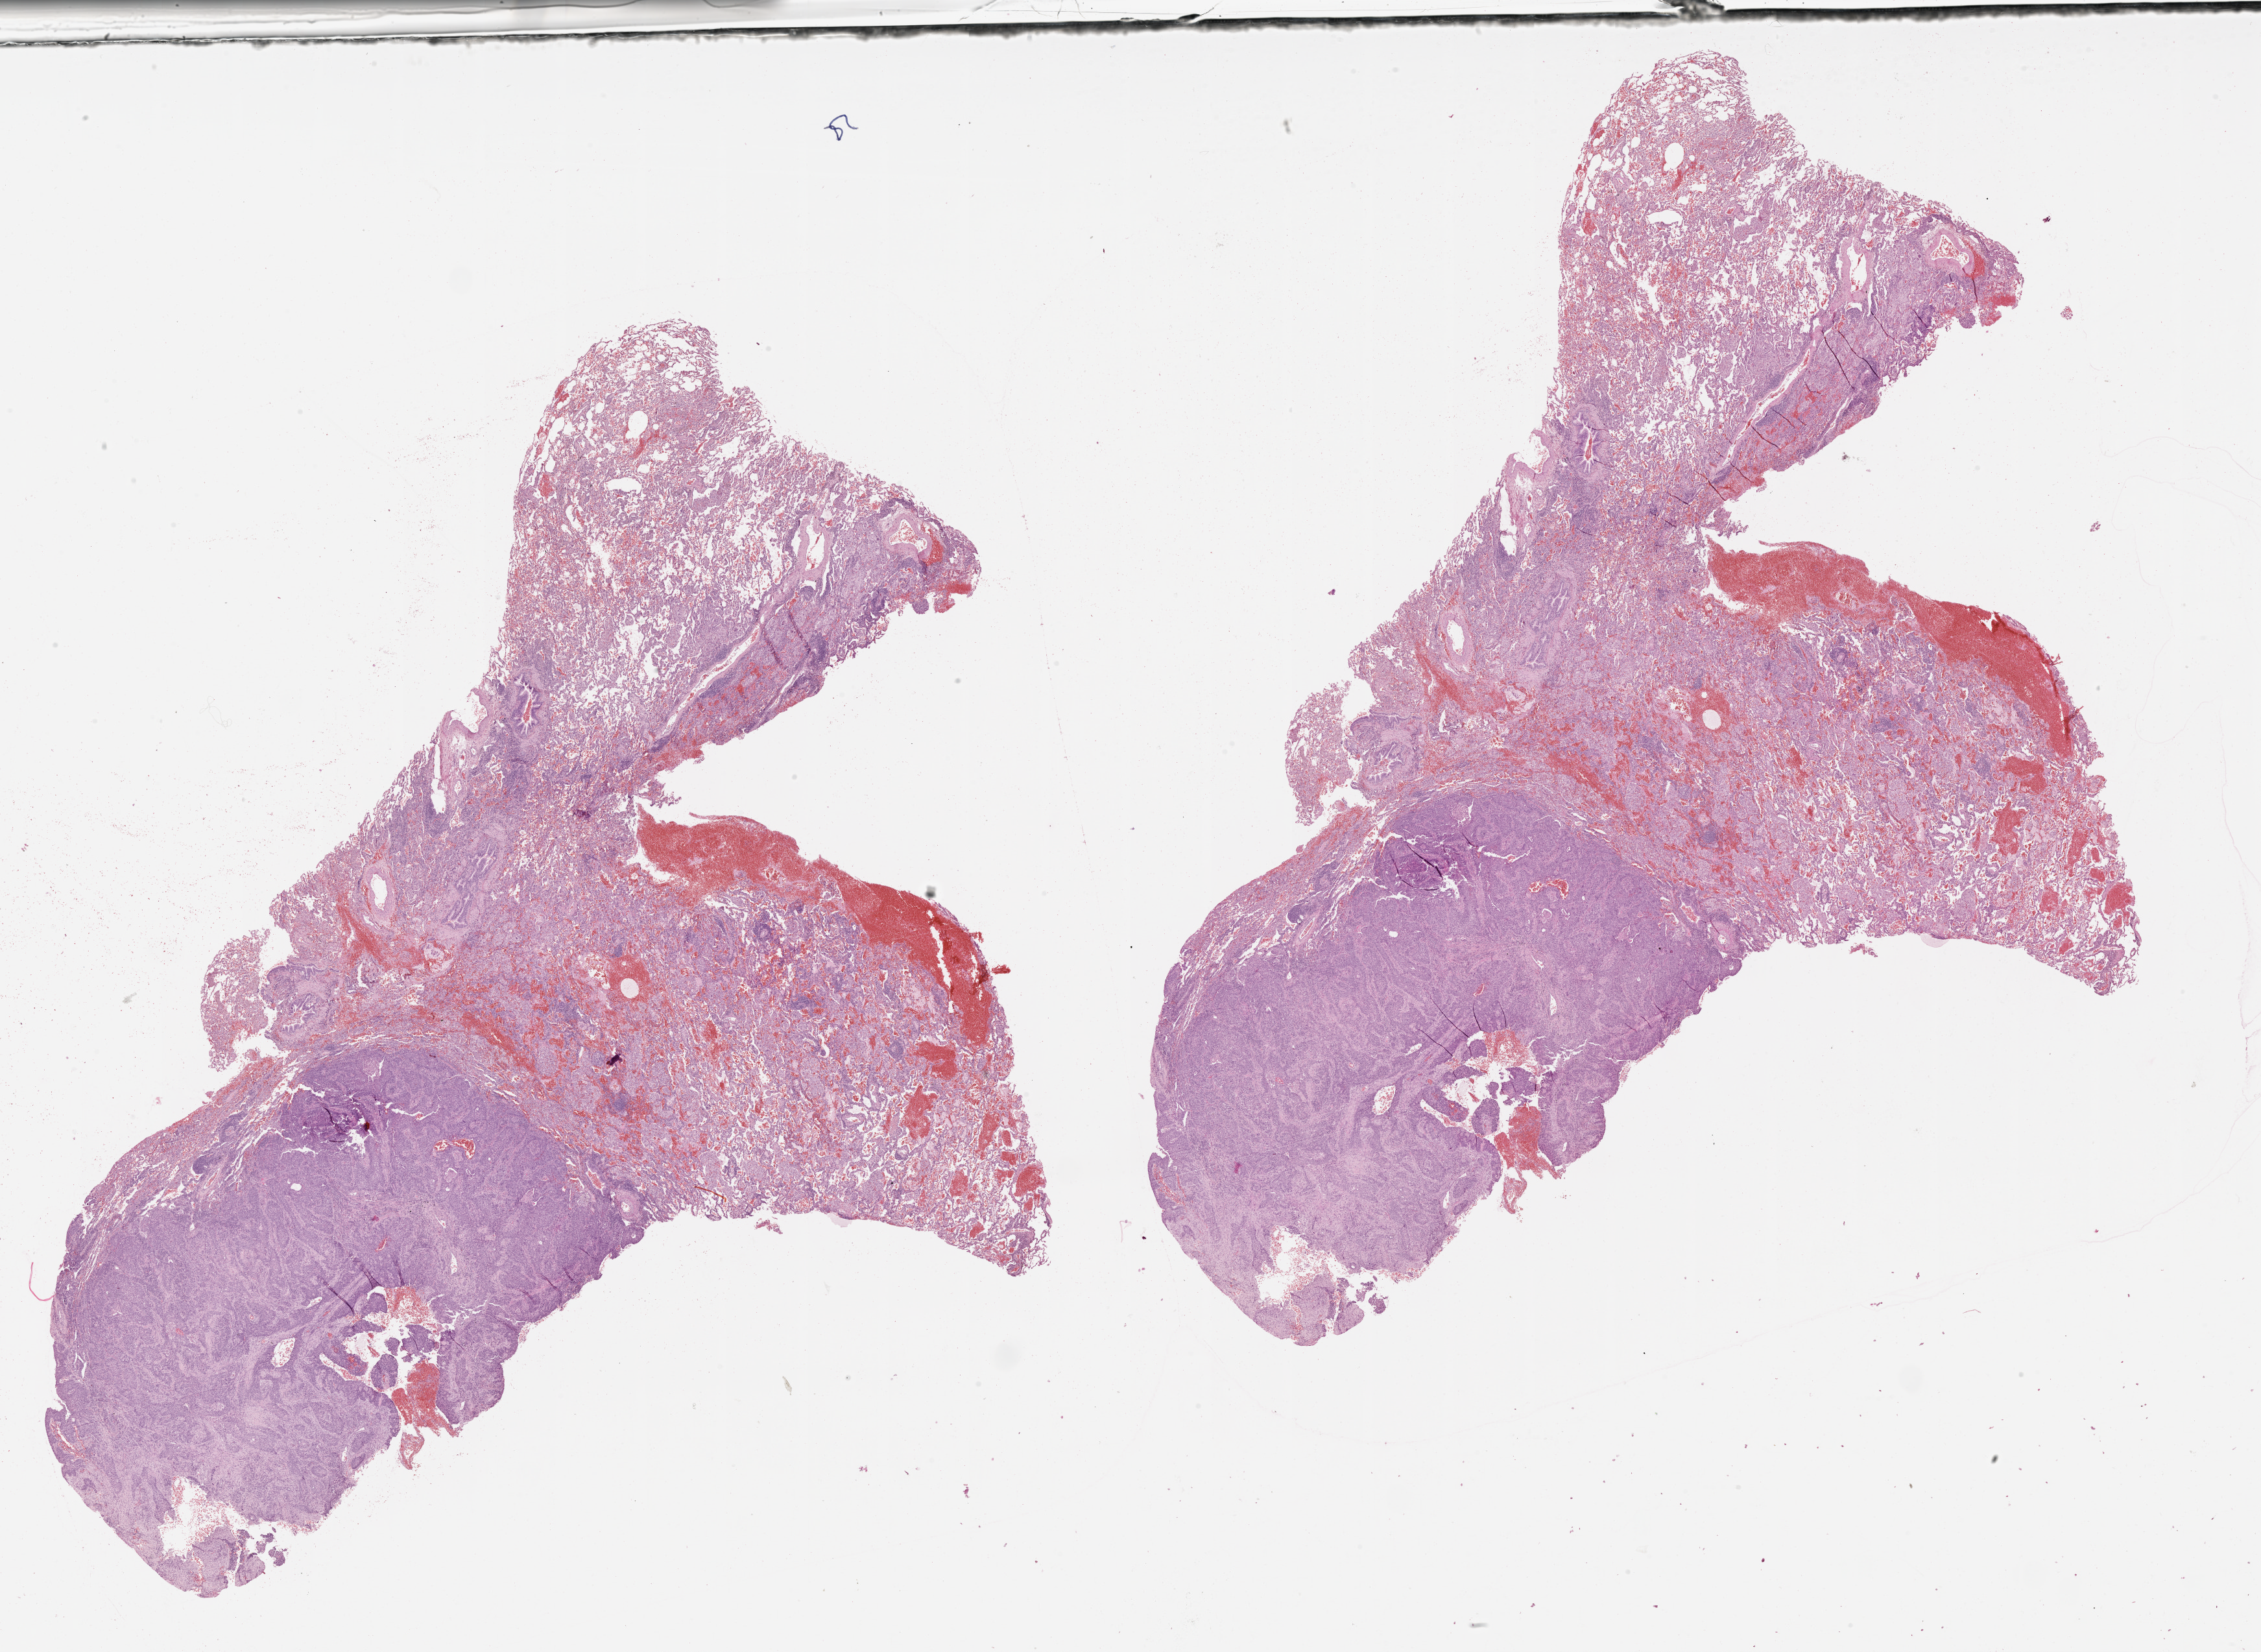
Whole-slide histology image, H&E-stained — whole scanned area (about 28.1 x 20.5 mm) shown as a low-resolution overview. Tumour tissue sample, lung. Patient: male, age 69 years.
Patient diagnosis (cohort enrolment): squamous cell carcinoma (lung).